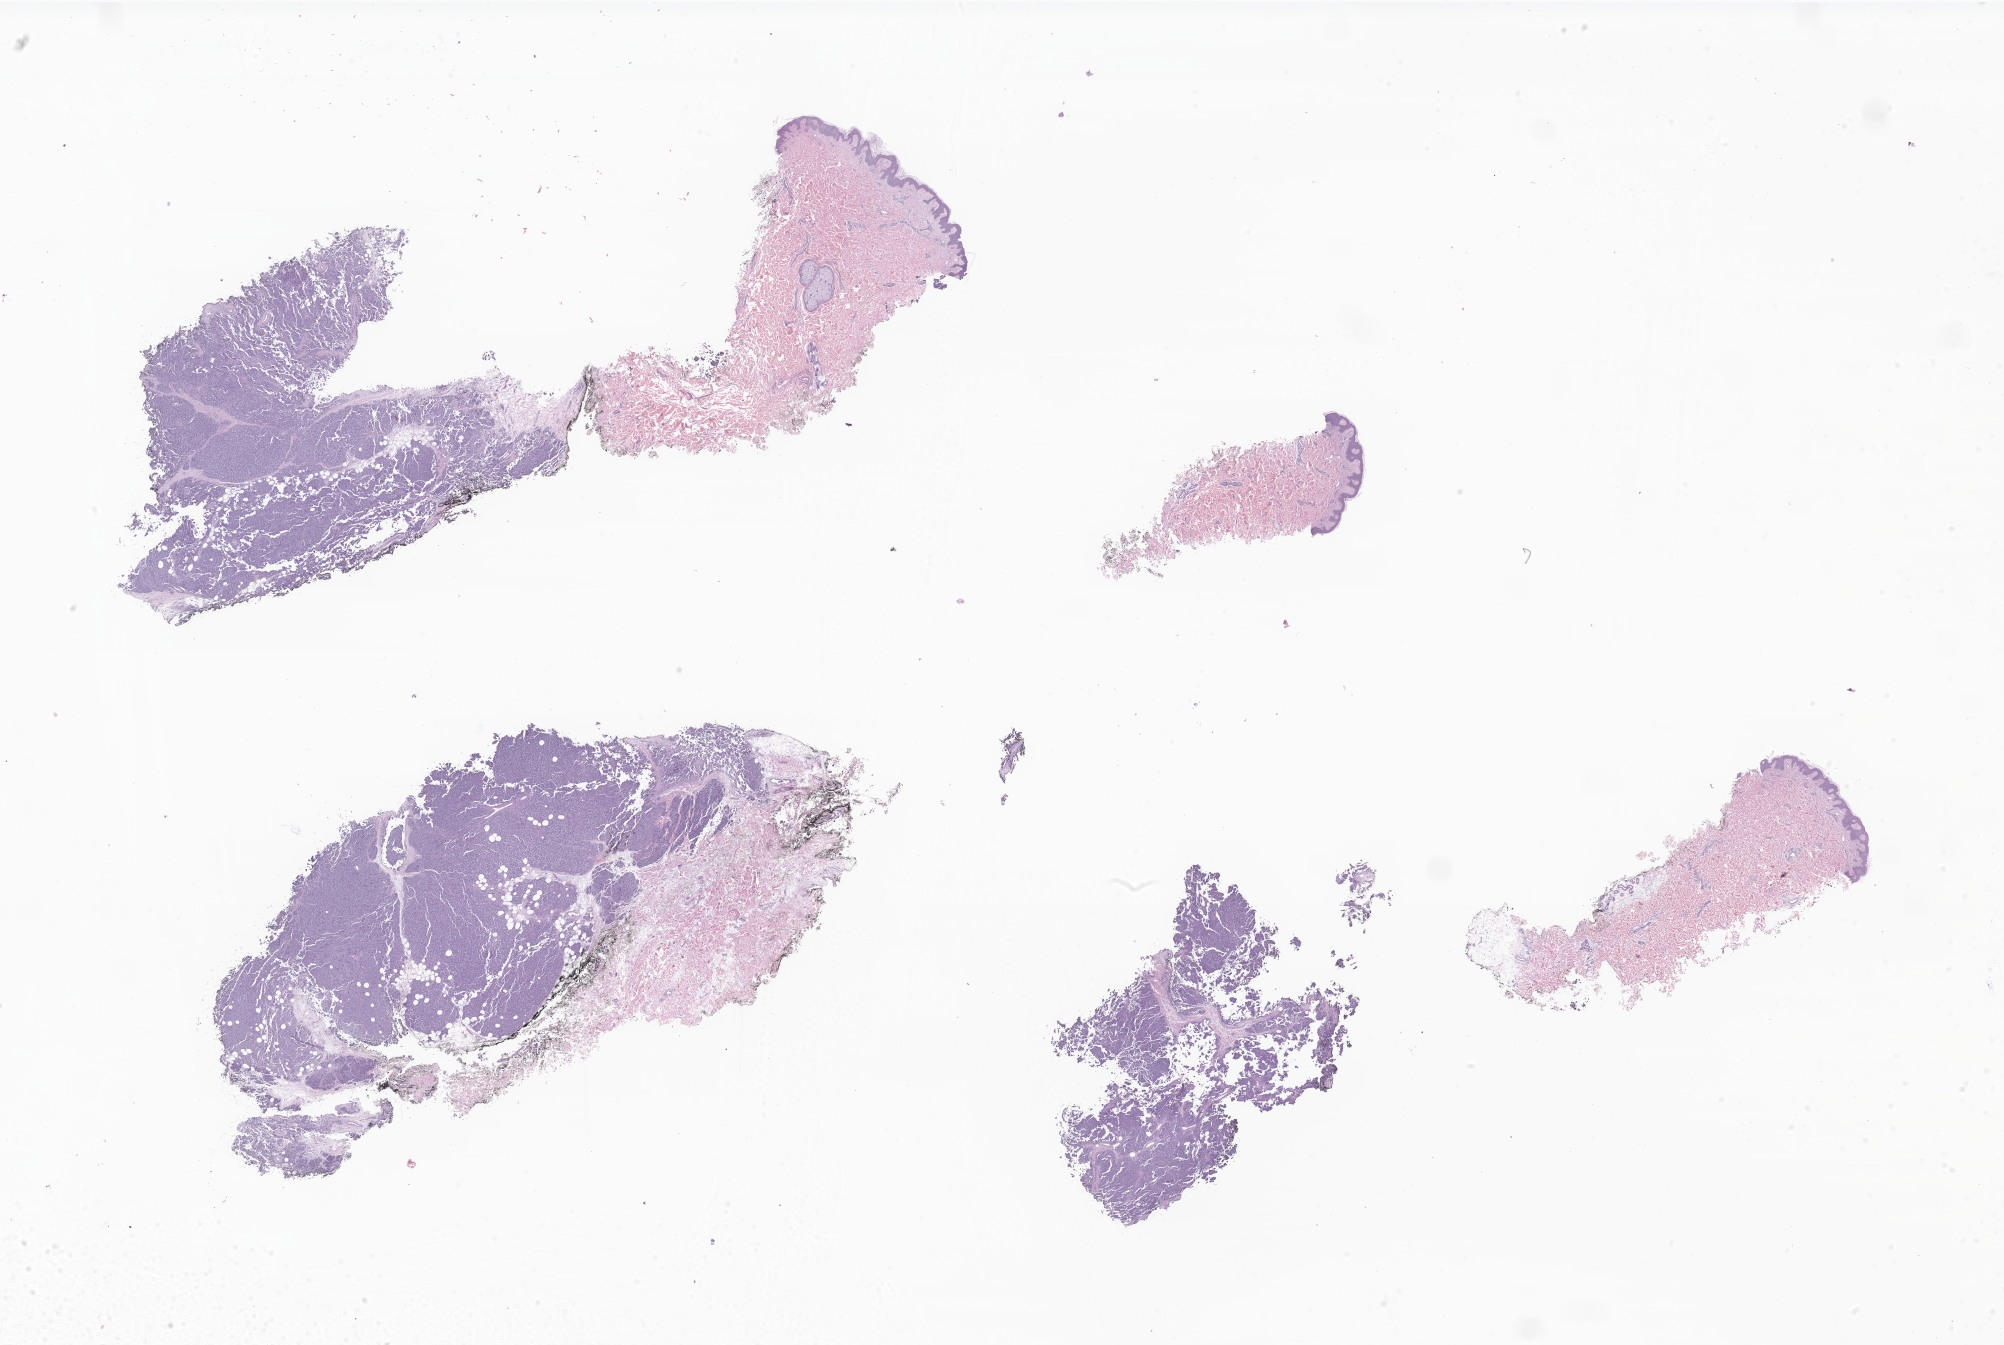
Hematoxylin and eosin (H&E) whole-slide image of tumor tissue from the soft tissue of upper extremity — whole scanned area (about 33.8 x 22.7 mm) shown as a low-resolution overview; FFPE section. Patient: male, age 248 months.
Diagnosis (ICD-O-3 morphology term): Ewing sarcoma.